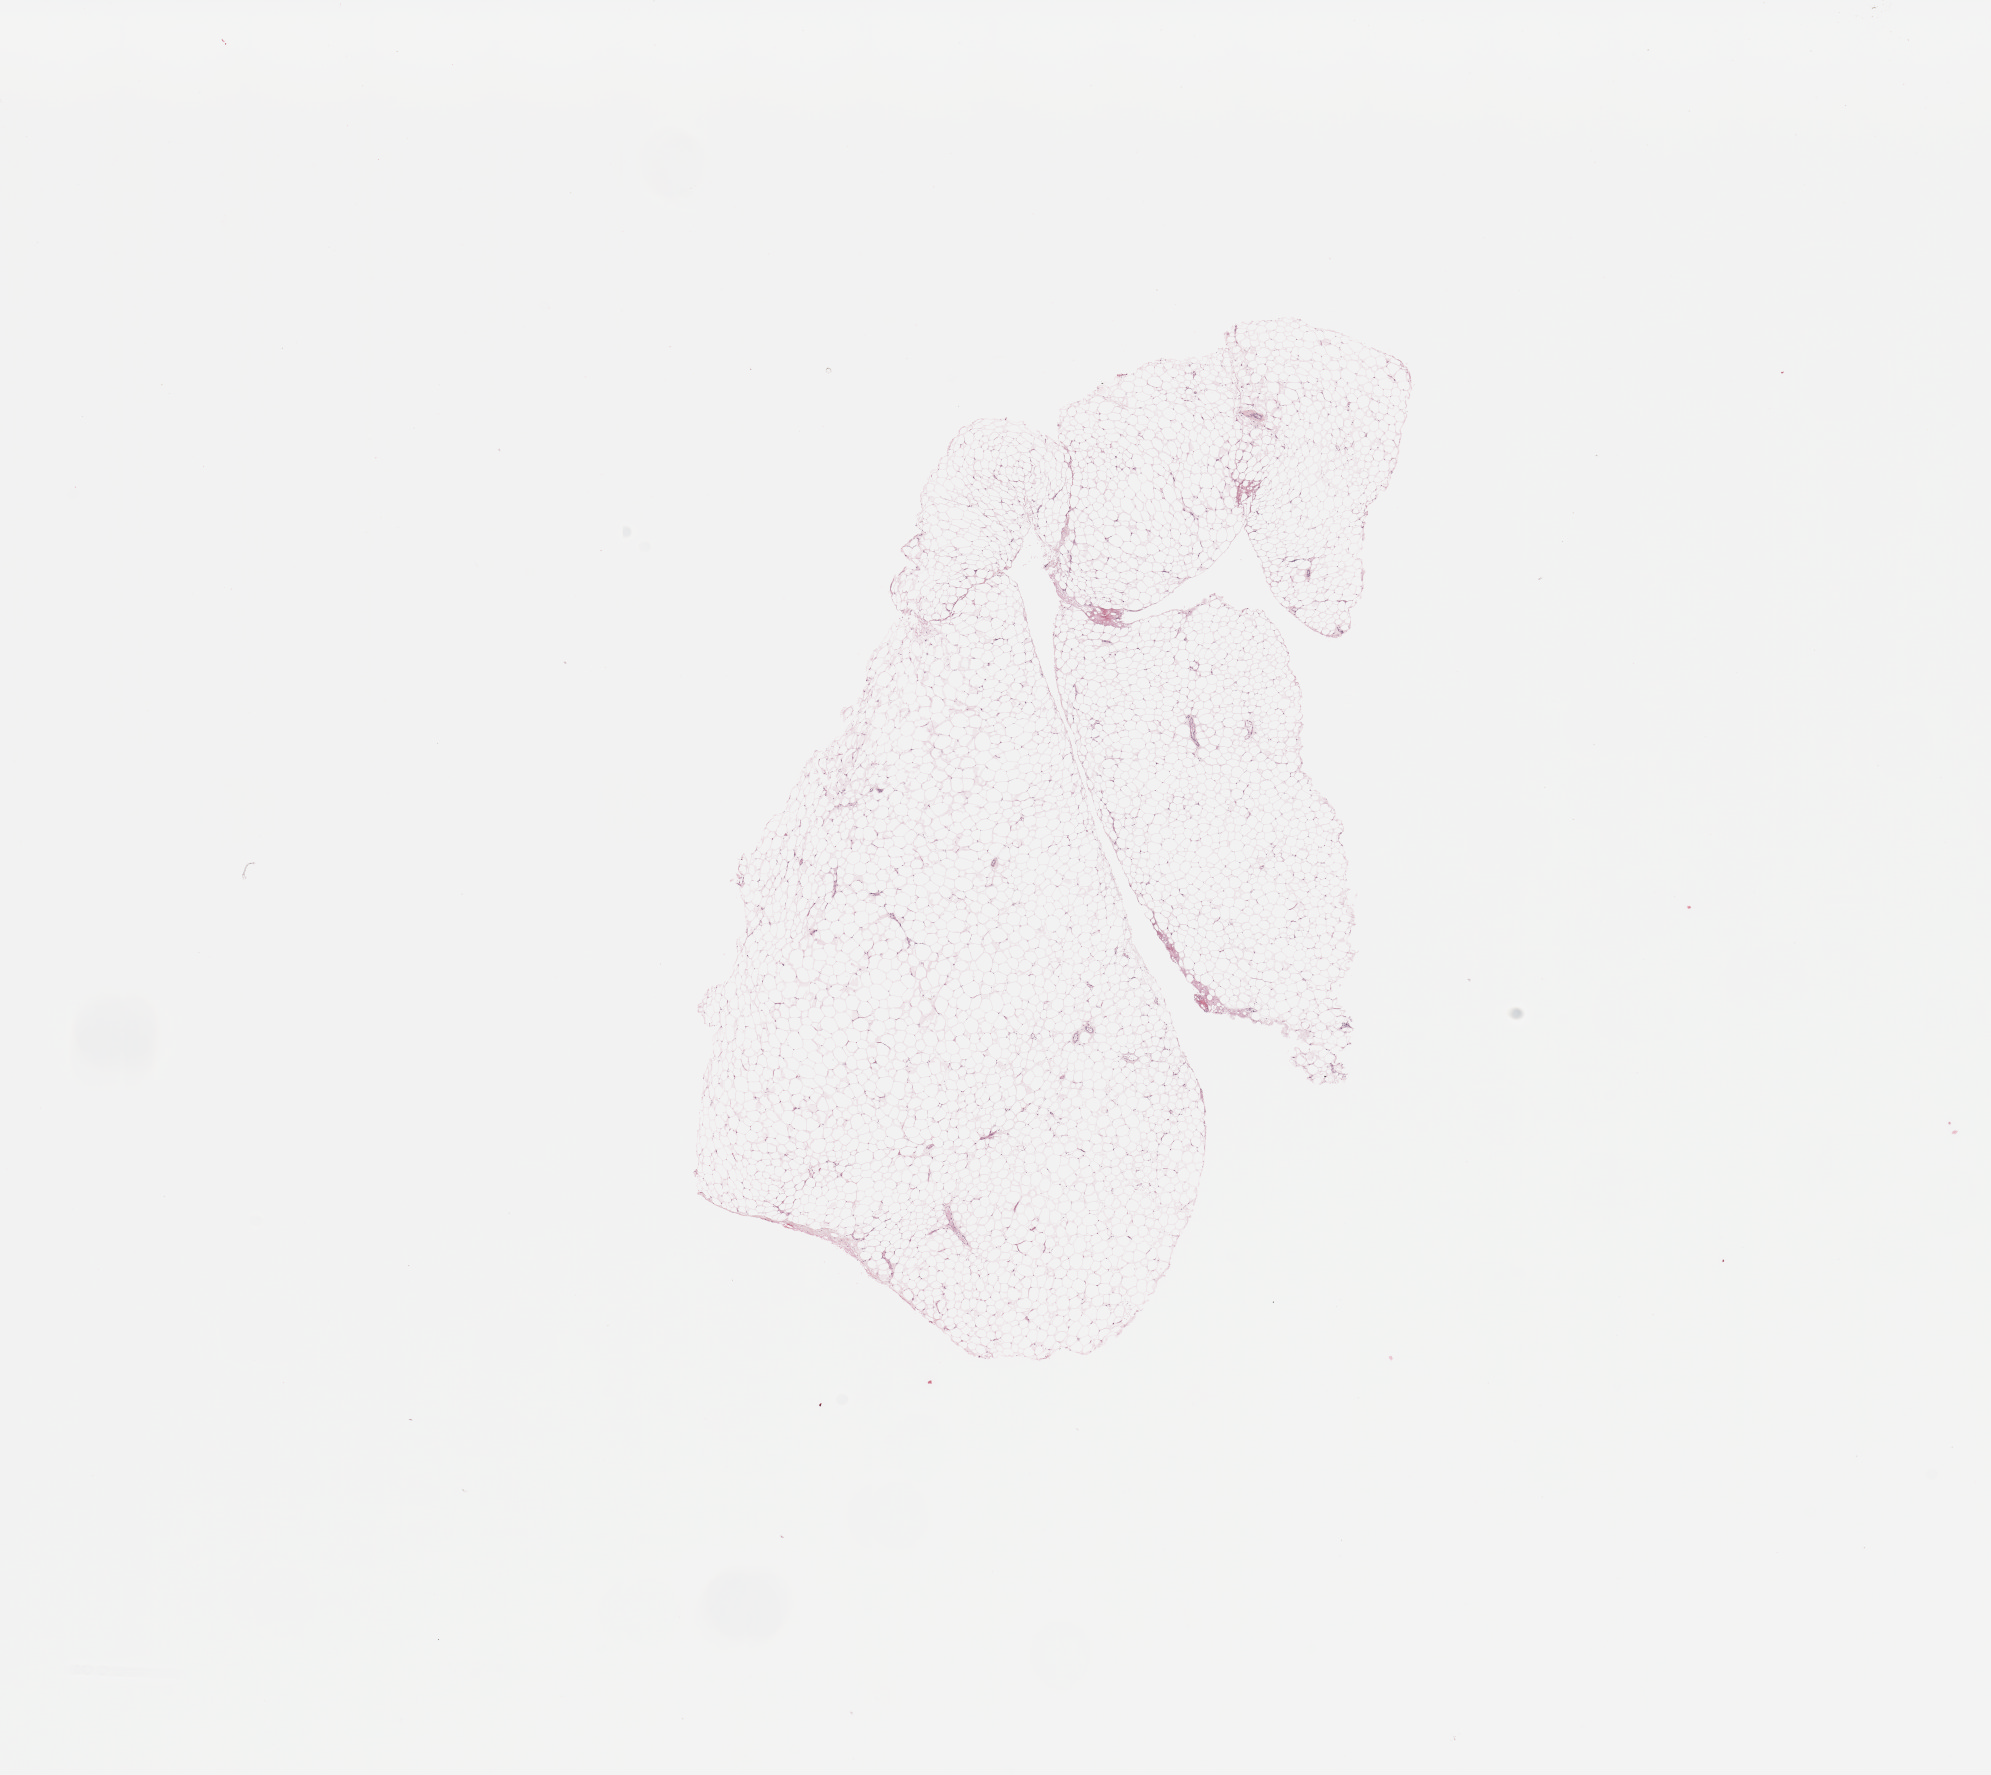
Digitized H&E tissue section (whole slide), low-resolution overview of the scanned area, about 15.8 x 14.0 mm, kidney, normal (non-tumour) tissue. Patient: male, age 67 years.
This section: normal (non-tumour) tissue from the same patient. Patient diagnosis: Renal cell carcinoma, NOS.